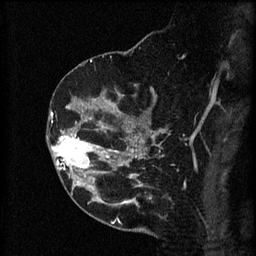
Breast MRI (dynamic contrast-enhanced), one sagittal slice. Position 37 of 60 along the scan axis. 3 images stored at this slice position (order not interpretable as contrast timing). 1.5 T. TE 4.2 ms, TR 8.2 ms. 2 mm slice thickness. 256 × 256 image matrix. Female patient, age 49 years.
Structures marked on this image (semi-automatic segmentation, software-assisted and operator-edited):
- analysis volume of interest (the breast-tissue region the enhancement analysis was run in; not a lesion): bounding box [x1, y1, x2, y2] px = [46, 126, 105, 177]
- tumour enhancement mask (voxels above the 70 % enhancement threshold inside the analysis volume of interest): [51, 130, 105, 177]